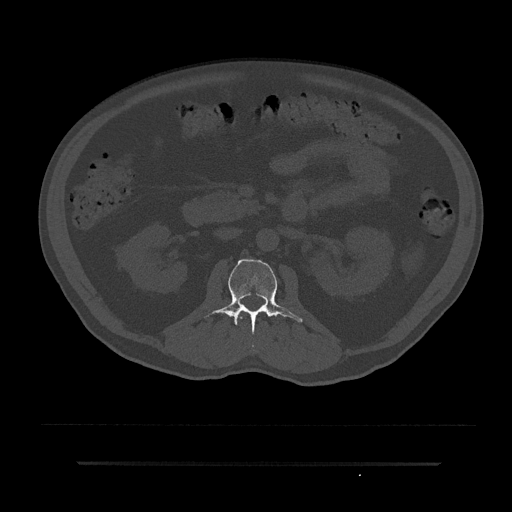
CT including the spine, one axial slice. Reconstruction kernel Br40s/3. Bone window (W 1800 / L 400 HU). 0.5 mm slice thickness. 512 × 512 image matrix. Patient: male, 59 years. From the clinical record (not read from this slice): primary cancer: bile ducts.
Structures marked on this image (semi-automatic segmentation, software-assisted and operator-edited):
- L1 vertebra: box from (x=236, y=311) to (x=243, y=326) px
- L2 vertebra: (x=204, y=259)–(x=303, y=333)